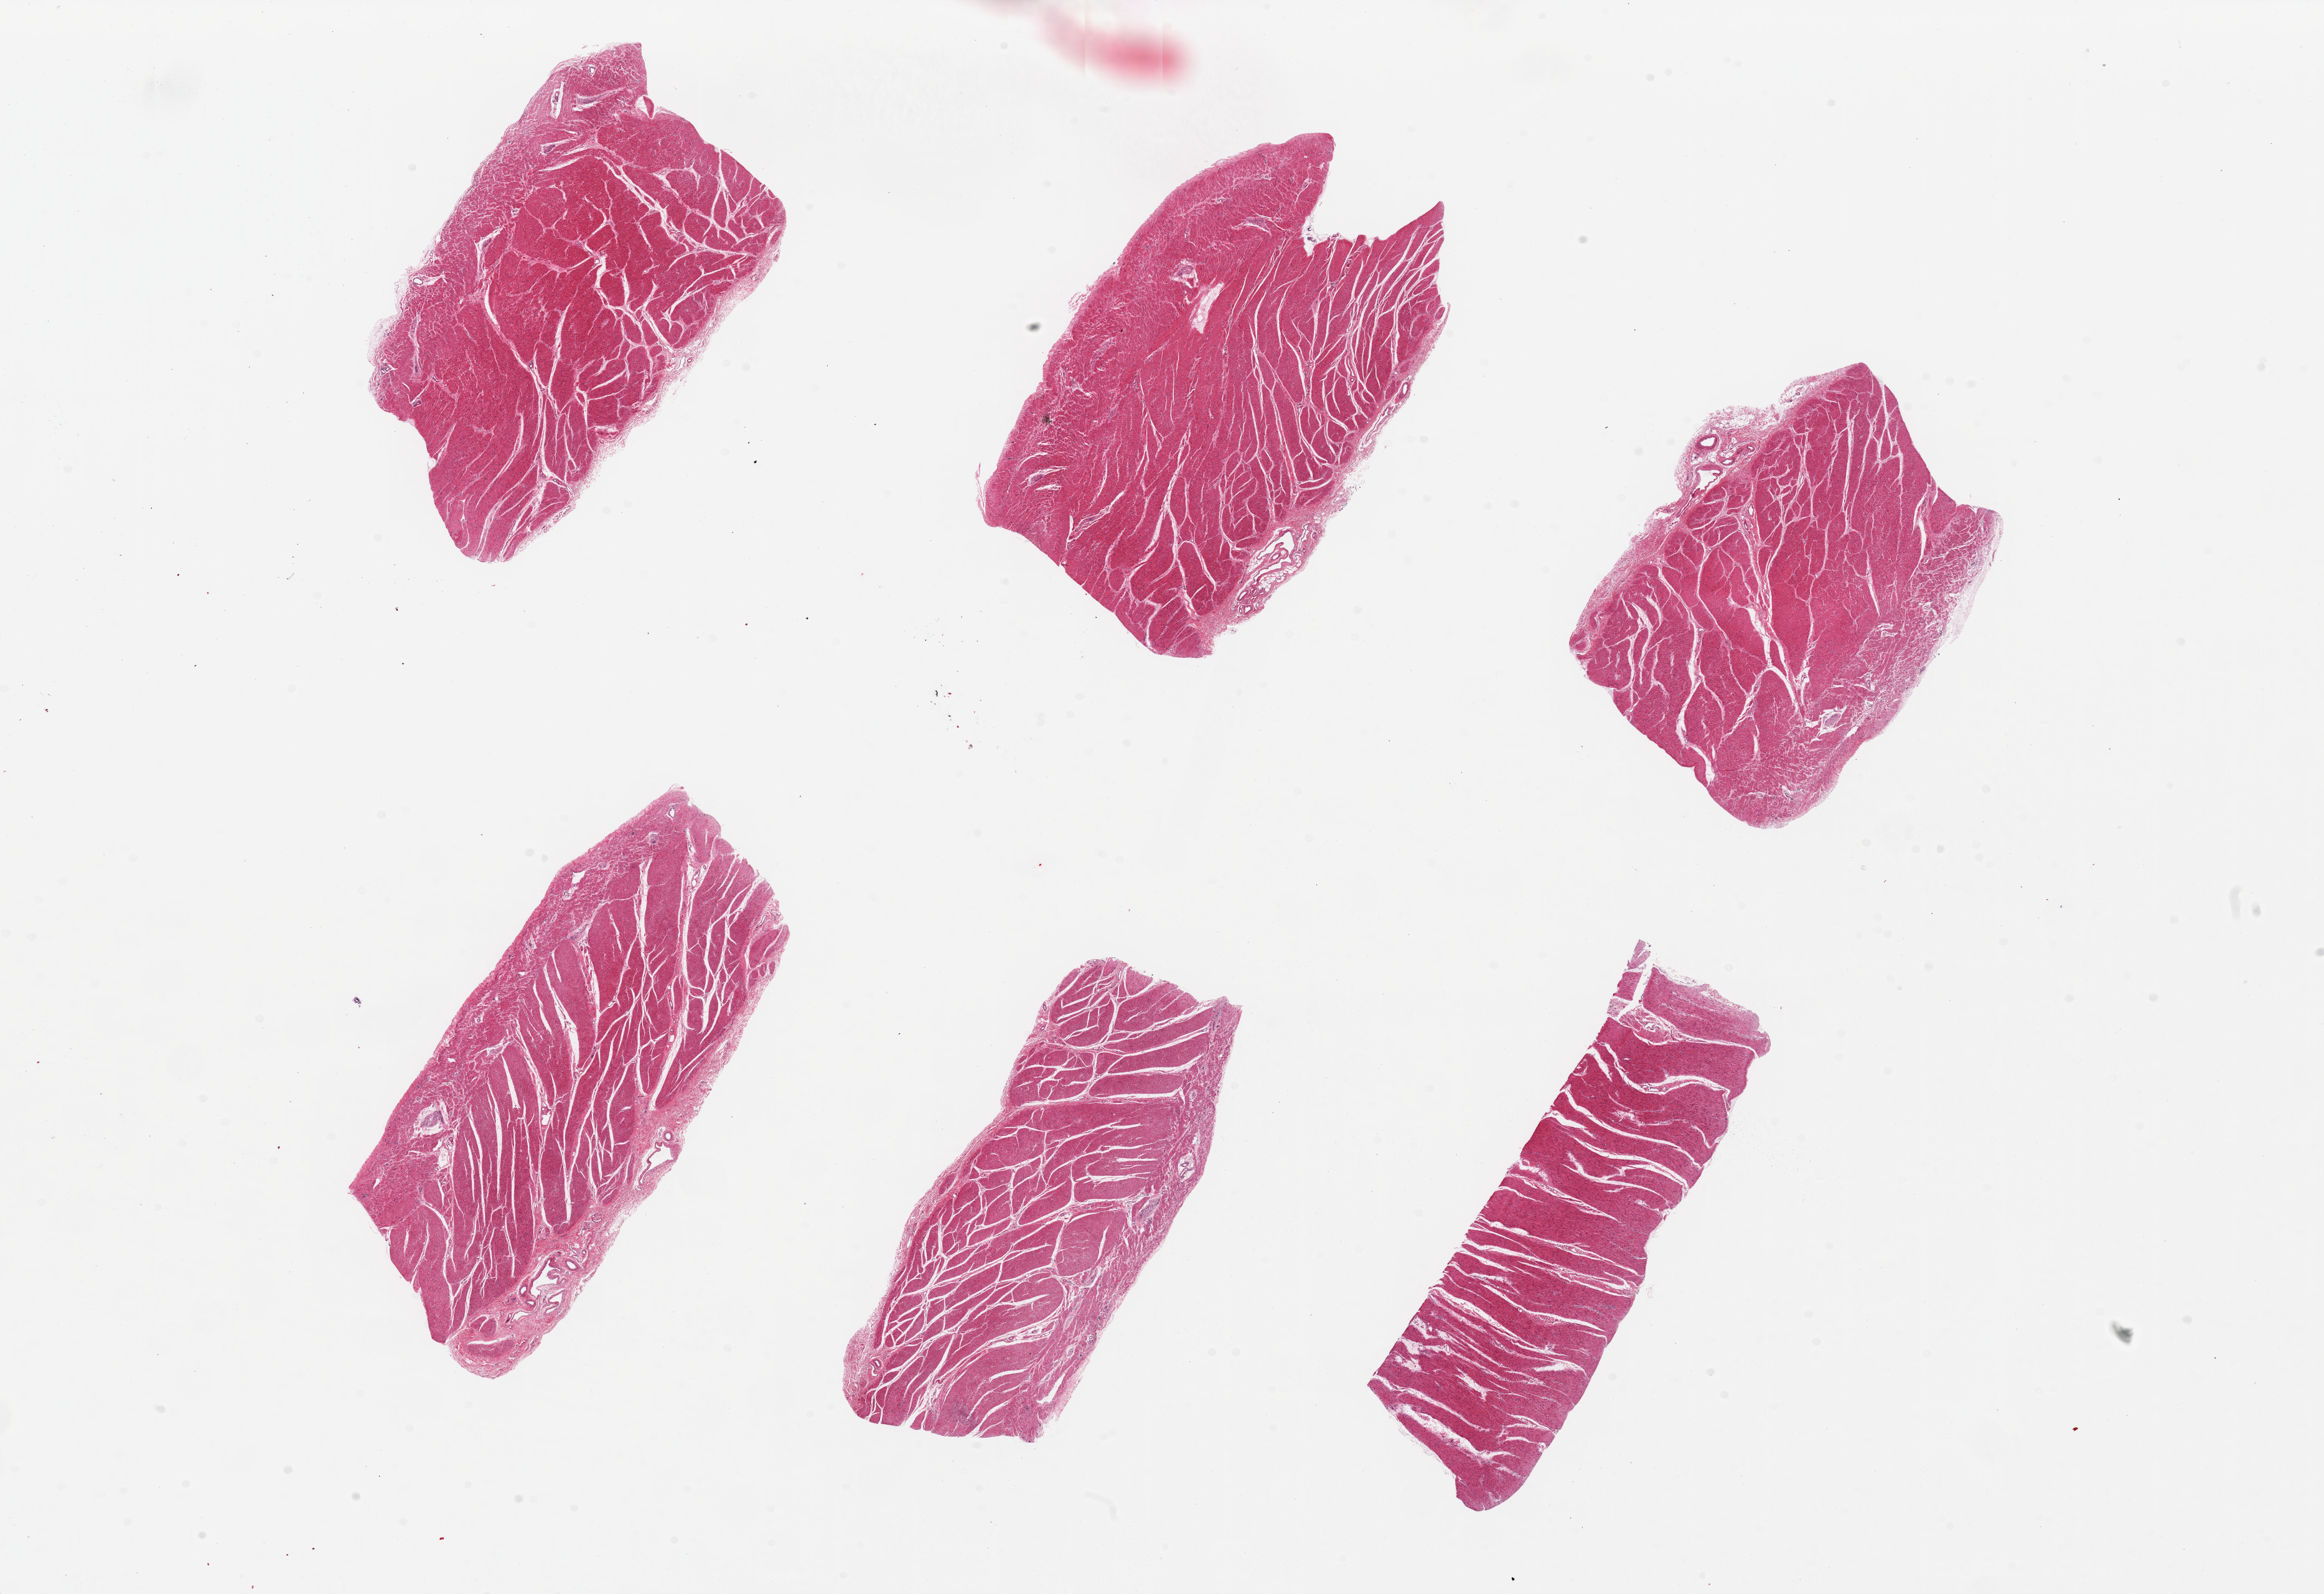
Whole-slide image, haematoxylin and eosin stain — low-resolution overview of the scanned area, about 29.5 x 20.3 mm (acquisition: 20x scan), PAXgene-fixed, paraffin-embedded tissue, target tissue: sigmoid colon, tissue donor sample. Donor sex: female.
• pathologist's review note for this sample: 6 pieces, up to 7x3mm; all muscularis, good specimens